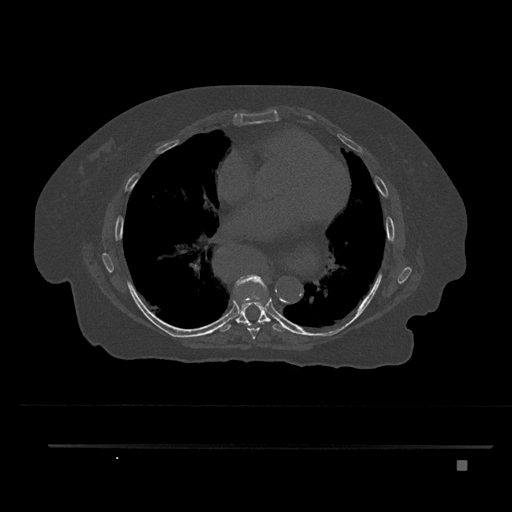
CT including the spine, one axial slice. Slice 462 of 797 in the series (ordered by position). Reconstruction kernel Br40s/3. Bone window (W 1800 / L 400 HU). 0.5 mm slice thickness. 512 × 512 image matrix. Patient: female, 76 years. From the clinical record (not read from this slice): primary cancer: lung.
Structures marked on this image (semi-automatically segmented with operator editing):
- T7 vertebra: bounding box <235,274,267,339> (left, top, right, bottom; pixels)
- T8 vertebra: <219,294,289,332>